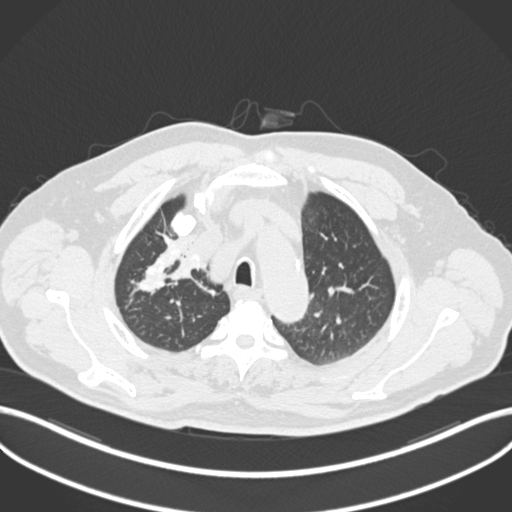
Chest CT, one axial slice. Position 162 of 255 along the scan axis. Reconstruction kernel B30f. Lung window (W 1500 / L -600 HU). 1 mm slice thickness. 512 × 512 image matrix, field of view 400 × 400 mm. Patient: male, 60 years. Case-level facts recorded for this patient, not image findings: clinical TNM (as recorded): T1b N1 M0.
Outlined on this slice (bounding box drawn by a radiologist):
- lung tumour (recorded histology: squamous cell carcinoma): bounding box [x1, y1, x2, y2] px = [158, 252, 205, 287]